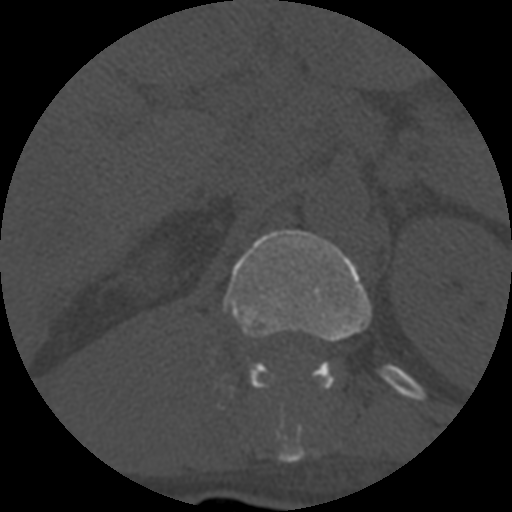
CT including the spine, one axial slice; slice 308 of 708 in the series (ordered by position); reconstruction kernel STANDARD; 120 kVp; one of 3 acquisitions stored at this slice position; bone window (W 1800 / L 400 HU); 1.25 mm slice thickness; 512 × 512 image matrix, field of view 160 × 160 mm. Patient age 55 years. From the clinical record (not read from this slice): primary cancer: colon.
Outlined on this slice (semi-automatic segmentation, software-assisted and operator-edited):
- T12 vertebra: bounding box <223,230,372,463> (left, top, right, bottom; pixels)